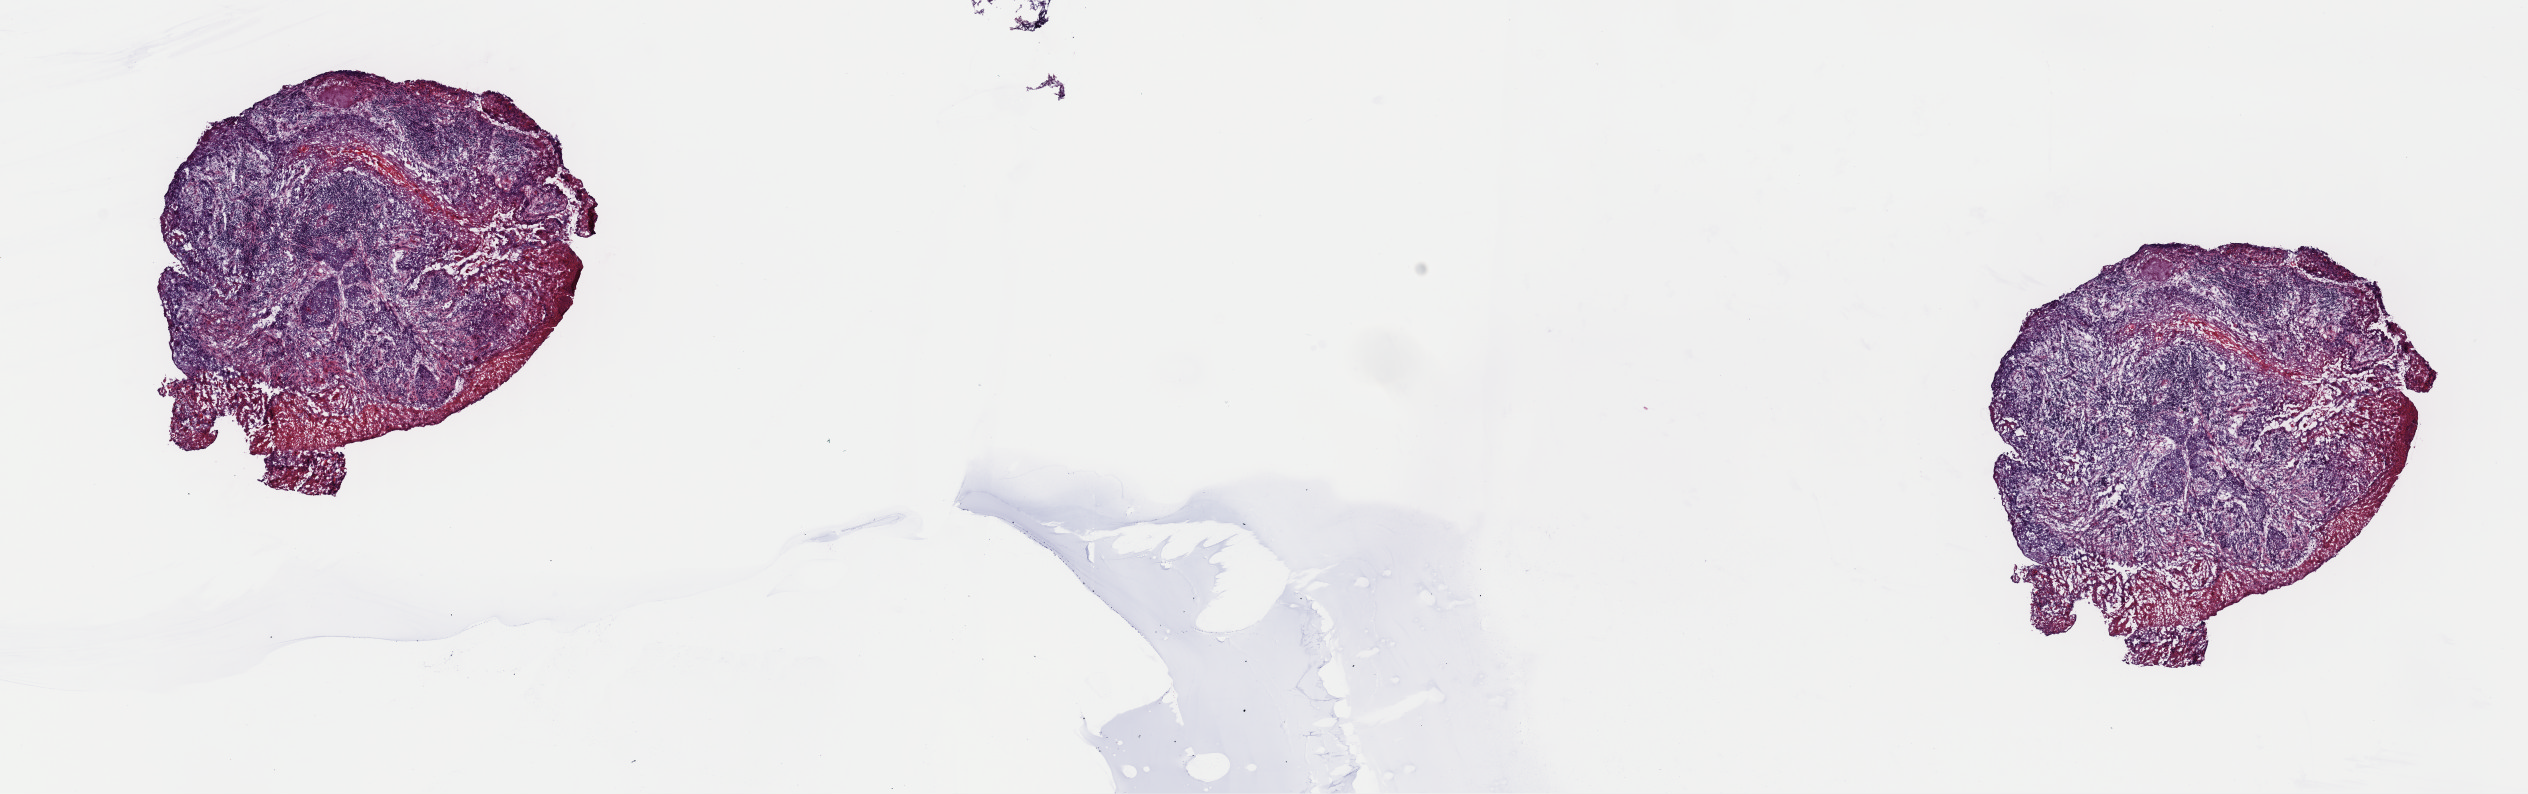
Hematoxylin and eosin (H&E) stained whole-slide image — low-resolution overview of the scanned area, about 20.0 x 6.3 mm. Frozen section. Sample: primary tumour, head and neck. Male patient; age at initial diagnosis 46 years. Histologic grade: G1 (well differentiated). Slide review estimates, as recorded: tumour cells 40%, tumour nuclei 80%, normal cells 0%, stromal cells 60%, necrosis 0%. Infiltration values recorded for this section: lymphocyte infiltration 25%, monocyte infiltration 2%, neutrophil infiltration 0%.
Histologic diagnosis: Squamous cell carcinoma, NOS (oropharynx, NOS). AJCC pathologic stage: II.